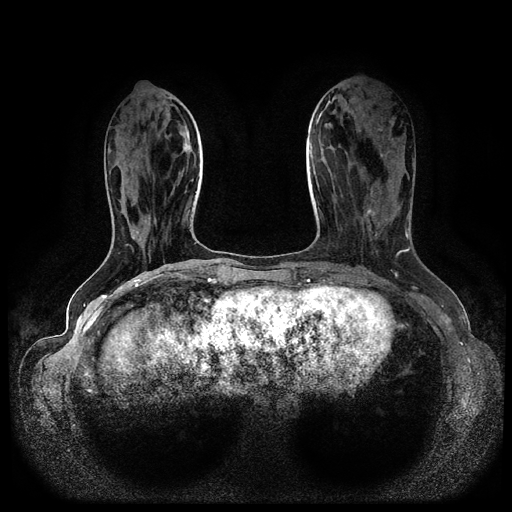
Breast MRI (dynamic contrast-enhanced, multi-phase), one axial slice; dynamic contrast-enhanced series, time point 2 of 5 at this slice position (early post-contrast); 1.5 T; TE 2.6 ms, TR 5.3 ms; 512 × 512 image matrix, field of view 350 × 350 mm. Female patient, age 45 years.
Outlined on this slice (semi-automatic segmentation, software-assisted and operator-edited):
- breast lesion (labelled 'tumour' in the annotation; benign lesions carry a separate 'benign' label): box from (x=363, y=204) to (x=381, y=236) px